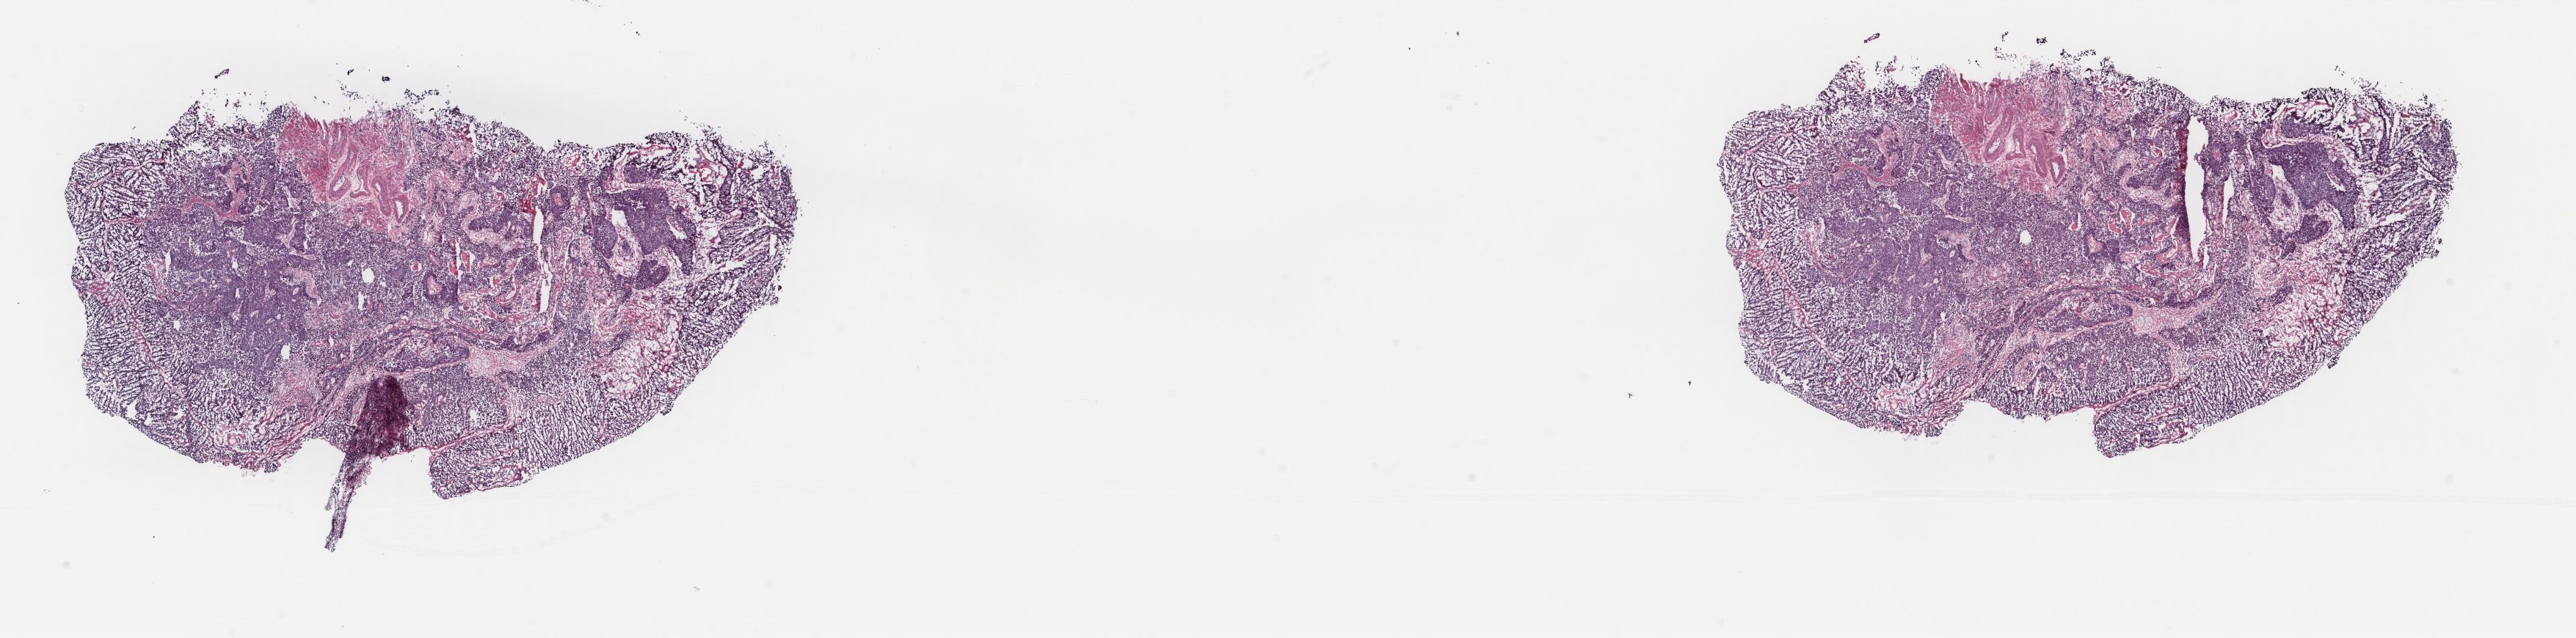
H&E whole-slide image — whole scanned area (about 27.9 x 6.9 mm, slide scanned at 40x) shown as a low-resolution overview. Frozen section. Primary tumour sample from the bladder. Male patient; age at initial diagnosis 67 years. Histologic grade: high grade. Slide review estimates, as recorded: tumour cells 80%, tumour nuclei 95%, normal cells 0%, stromal cells 18%, necrosis 2%. Inflammatory infiltration, as recorded: lymphocyte infiltration 2%, monocyte infiltration 0%, neutrophil infiltration 0%.
Histologic diagnosis: Papillary transitional cell carcinoma. AJCC pathologic stage: III (7th edition). Lymph nodes positive (case pathology): 0 of 7 examined. TNM: T4a N0 M0.